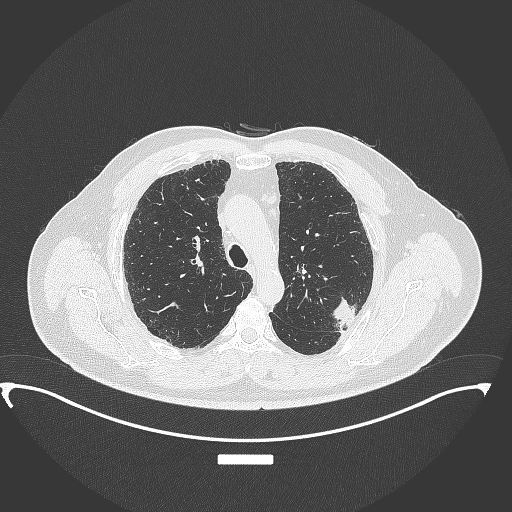
Chest CT, one axial slice; position 259 of 350 along the scan axis; reconstruction kernel B70f; lung window (W 1500 / L -600 HU); 512 × 512 image matrix. Patient: male, 64 years. From the clinical record (not read from this slice): clinical TNM (as recorded): T1c N1 M1.
Structures marked on this image (bounding box drawn by a radiologist):
- lung tumour (recorded histology: adenocarcinoma): bounding box (x1, y1, x2, y2) in pixels: (330, 294, 365, 333)